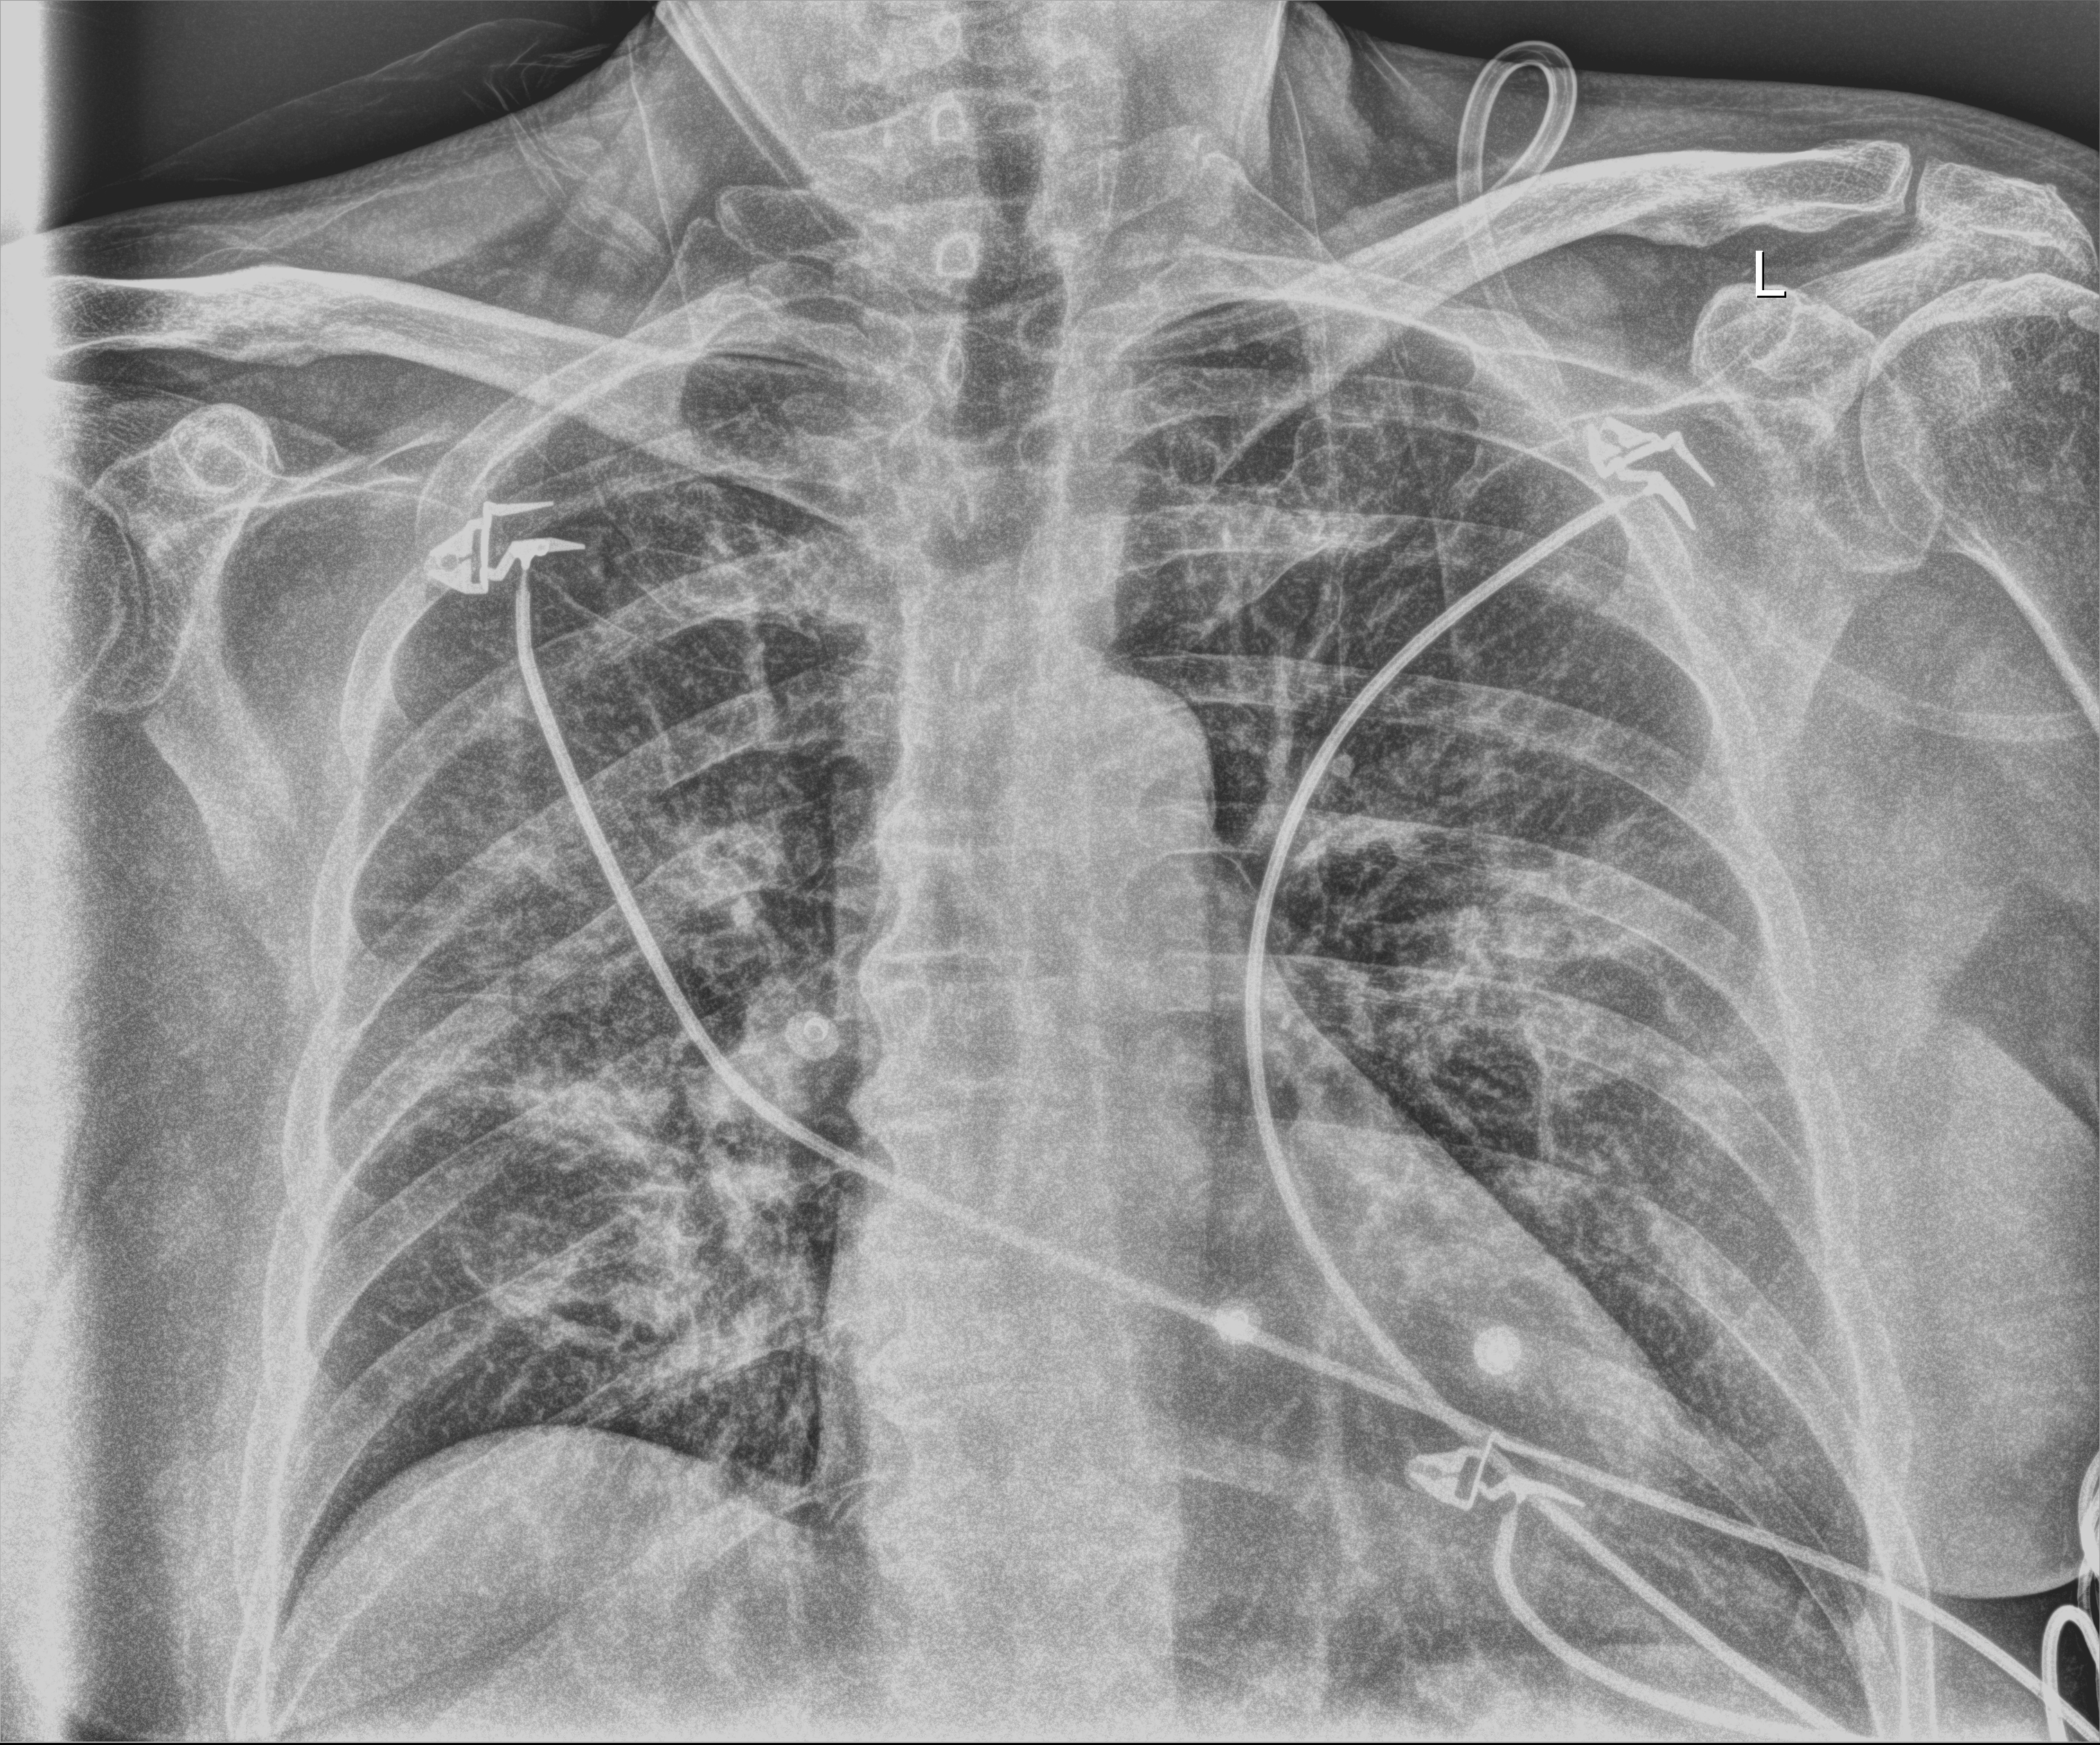
Chest X-ray (portable), anteroposterior (AP) projection. Male patient hospitalised with COVID-19, age 60–74 years.
Hospital-stay facts (about this admission, not read from this image; timing relative to this image not recorded):
- smoking status (admission record): never
- admitted to intensive care during this hospital stay: no